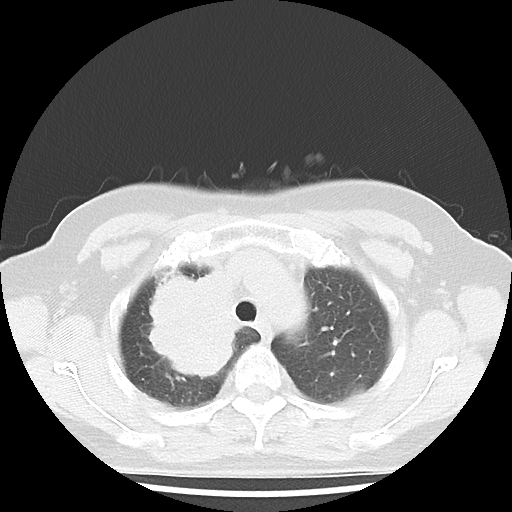
Chest CT, one axial slice; 100 kVp; lung window (W 1500 / L -600 HU); 5 mm slice thickness; 512 × 512 image matrix. Female patient, age 62 years. Case-level facts recorded for this patient, not image findings: clinical TNM (as recorded): T3 N0 M0.
Outlined on this slice (rectangle marked by the reading radiologist):
- lung tumour (recorded histology: small cell carcinoma): box from (x=132, y=259) to (x=240, y=387) px